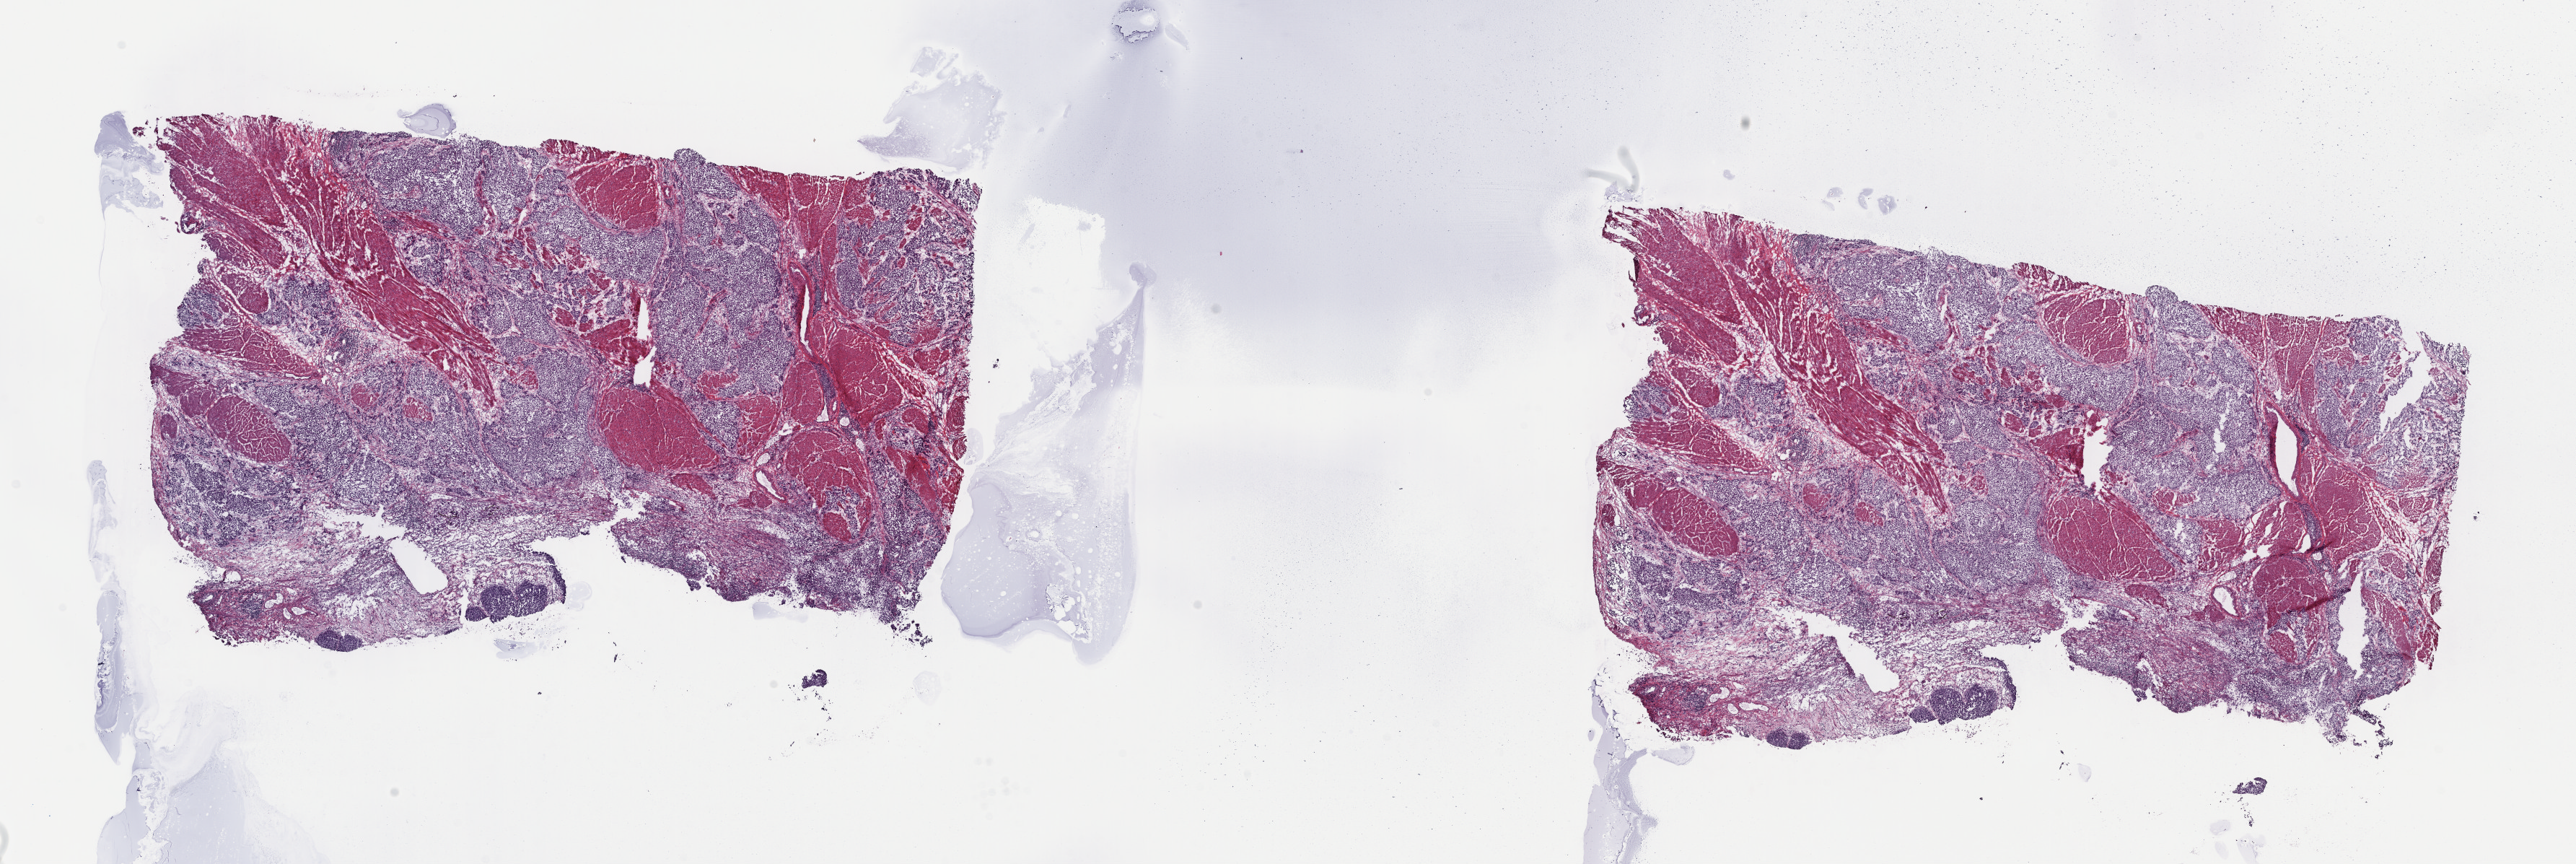
Whole-slide histology image, H&E-stained, low-resolution overview of the scanned area, about 28.2 x 9.4 mm (from a 40x scan), frozen section, bladder, primary tumour sample. Patient: male, age at initial diagnosis 61 years. Histologic grade: high grade. Pathologist review of this section (percent, as recorded): tumour cells 80%, tumour nuclei 80%, normal cells 0%, stromal cells 20%, necrosis 0%. Infiltration values recorded for this section: lymphocyte infiltration 5%, monocyte infiltration 2%, neutrophil infiltration 3%.
• diagnosis: Transitional cell carcinoma (posterior wall of bladder)
• AJCC pathologic stage: IV (7th edition)